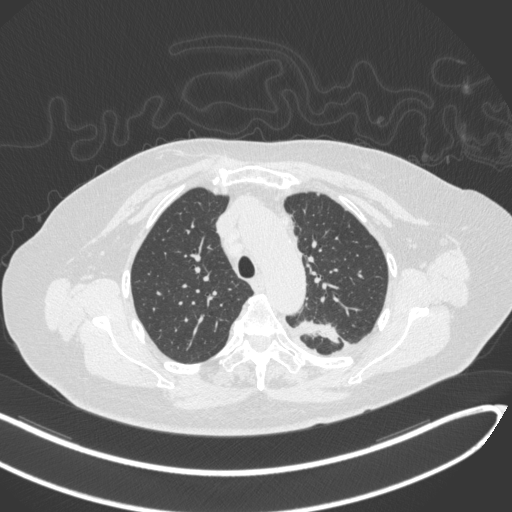
Chest CT, one axial slice. Position 236 of 270 along the scan axis. Reconstruction kernel B31f. 120 kVp. Lung window (W 1500 / L -600 HU). 512 × 512 image matrix, field of view 400 × 400 mm. Patient: female, 76 years. Case-level facts recorded for this patient, not image findings: clinical TNM (as recorded): T1c N0 M0.
Structures marked on this image (rectangle marked by the reading radiologist):
- lung tumour (recorded histology: adenocarcinoma): bounding box (x1, y1, x2, y2) in pixels: (290, 313, 341, 346)